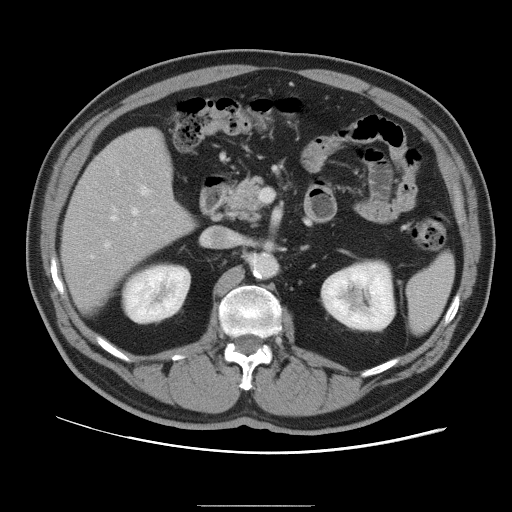
Contrast-enhanced abdominal CT, one axial slice; slice 49 of 105 in the series (ordered by position); 120 kVp; soft-tissue window (W 400 / L 40 HU); 5 mm slice thickness; 512 × 512 image matrix, field of view 399 × 399 mm. Male patient, age 64 years. Case-level facts recorded for this patient, not image findings: diagnosis: colorectal cancer liver metastases, imaged before liver resection; multiple liver metastases: yes; largest metastasis: 3 cm; disease in both lobes: yes.
Outlined on this slice (outlined manually by an expert reader):
- hepatic veins: bounding box (x1, y1, x2, y2) in pixels: (91, 208, 138, 259)
- liver: (63, 129, 194, 311)
- planned liver remnant (the part of the liver to remain after resection): (63, 130, 193, 311)
- portal vein (with intrahepatic branches): (105, 185, 151, 247)